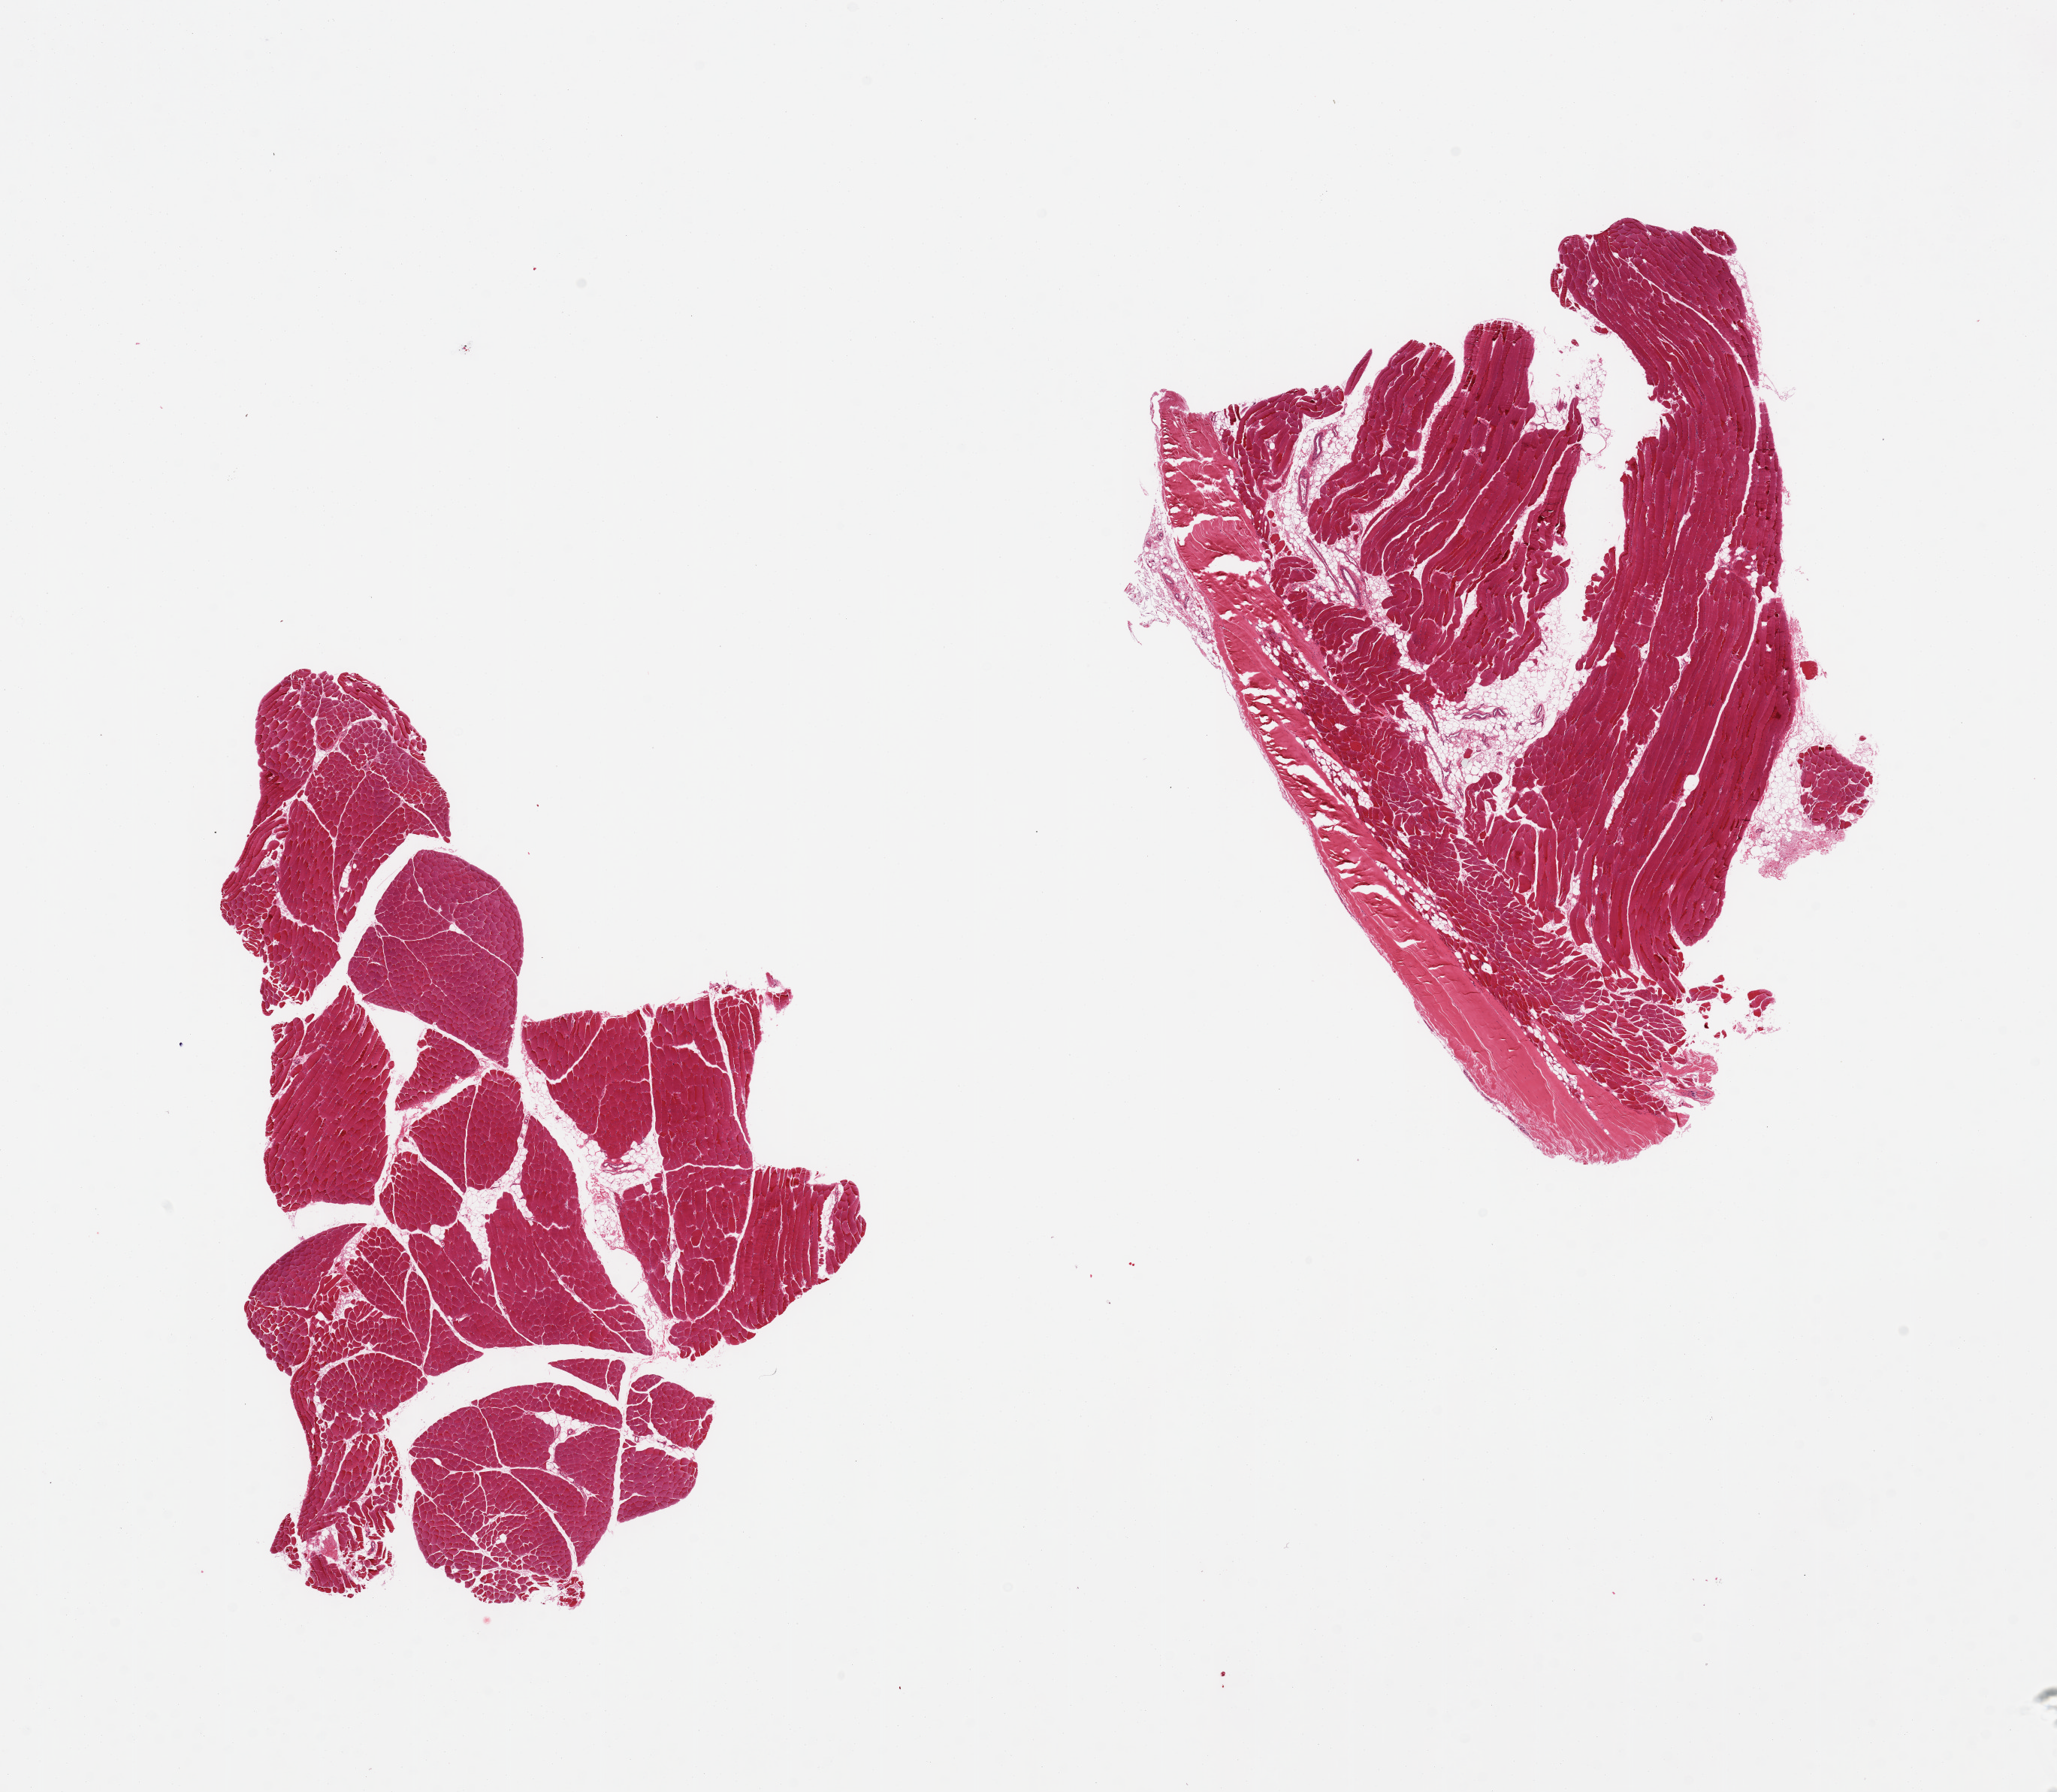
Hematoxylin and eosin (H&E) whole-slide image, a low-resolution overview of the entire scanned area, about 21.7 x 18.9 mm; PAXgene-fixed paraffin-embedded (PFPE) section; target tissue: skeletal muscle; tissue donor sample. Female donor.
Reviewer comment on this tissue sample: 2 pieces; 10-20% internal fat; 20% tendon in 1 piece.